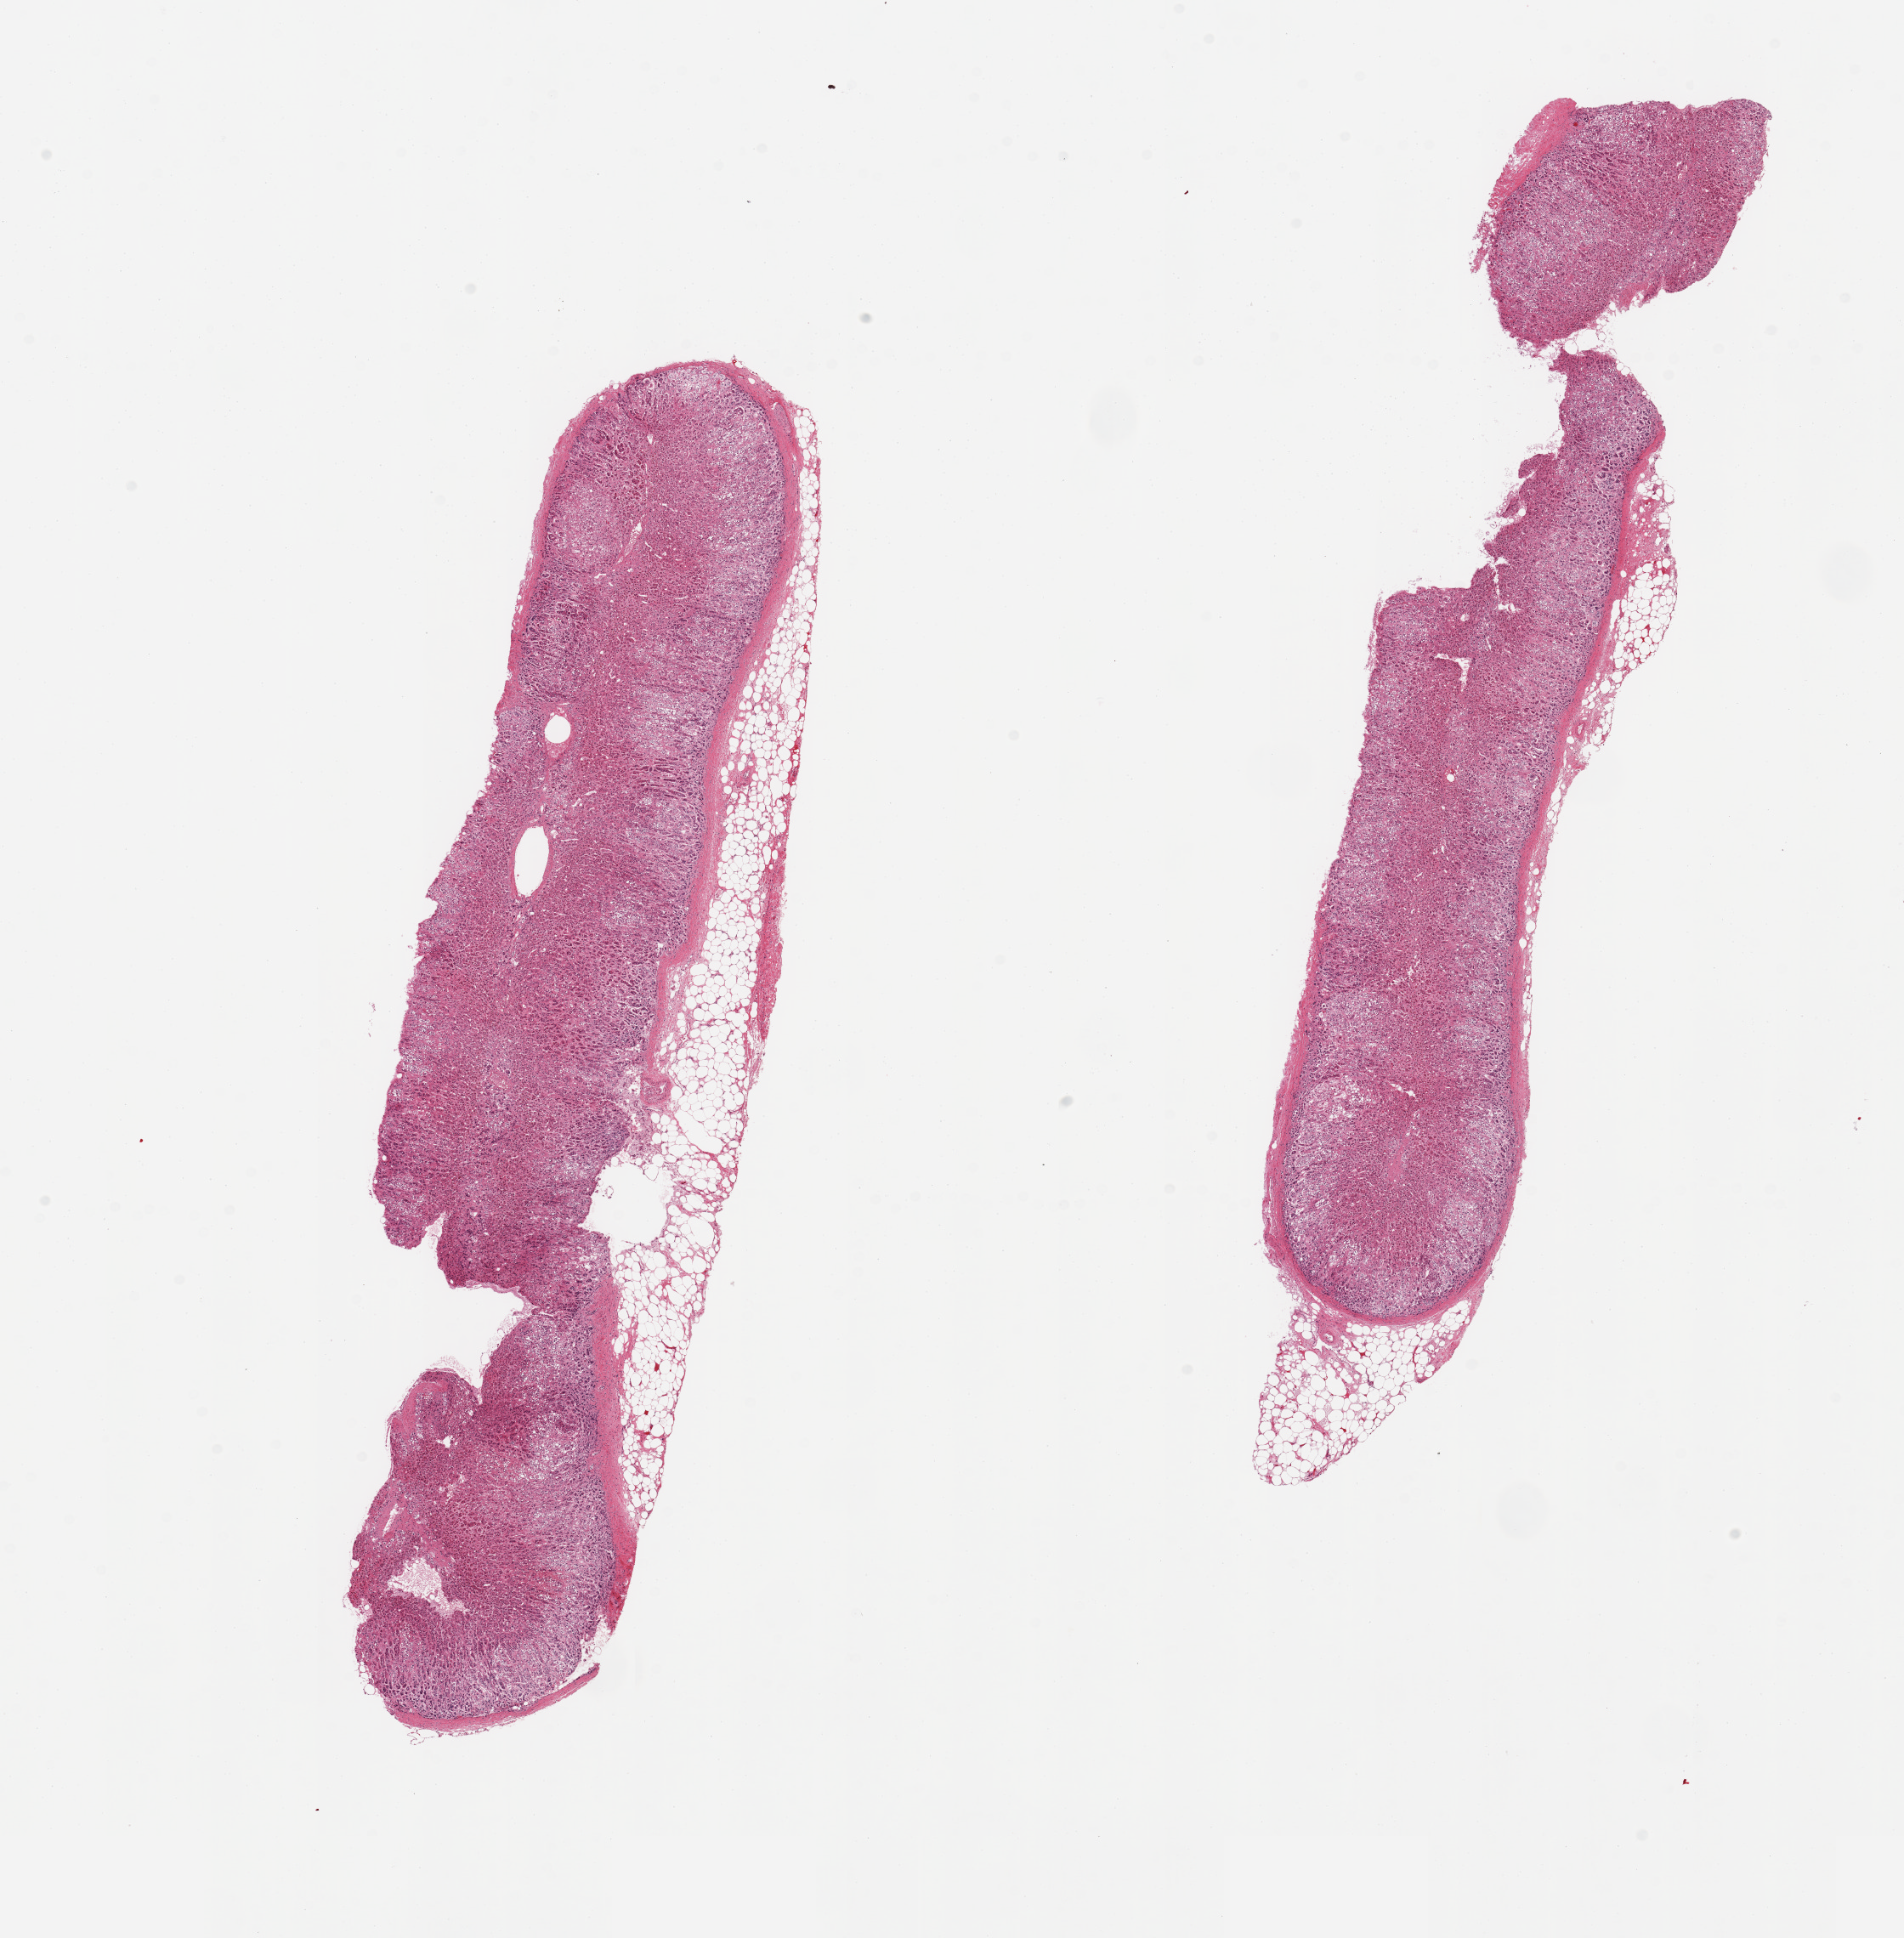
Whole-slide image, H&E stain — shown as a low-resolution overview of the whole scanned area (about 17.7 x 18.0 mm, from a 20x scan); PAXgene-fixed paraffin-embedded (PFPE) section; target tissue: adrenal gland; tissue donor sample.
Review note (as recorded): 2 pieces; 10 and 20% attached fat.